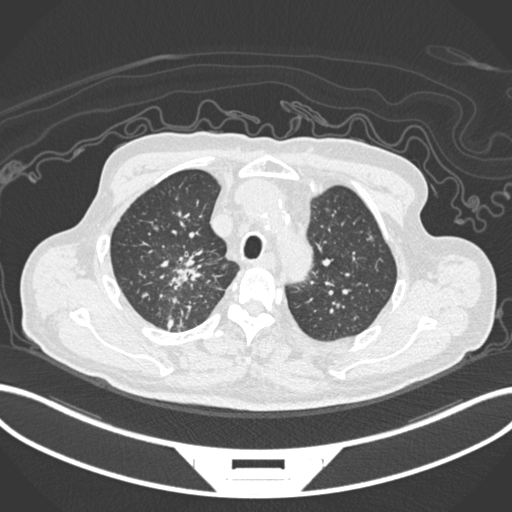
Chest CT, one axial slice; slice 168 of 207 in the series (ordered by position); reconstruction kernel B30f; lung window (W 1500 / L -600 HU); 1 mm slice thickness; 512 × 512 image matrix, field of view 400 × 400 mm. Patient: male, 69 years. From the clinical record (not read from this slice): clinical TNM (as recorded): T1c N1 M1.
Outlined on this slice (bounding box drawn by a radiologist):
- lung tumour (recorded histology: adenocarcinoma): bounding box [x1, y1, x2, y2] px = [159, 250, 206, 297]